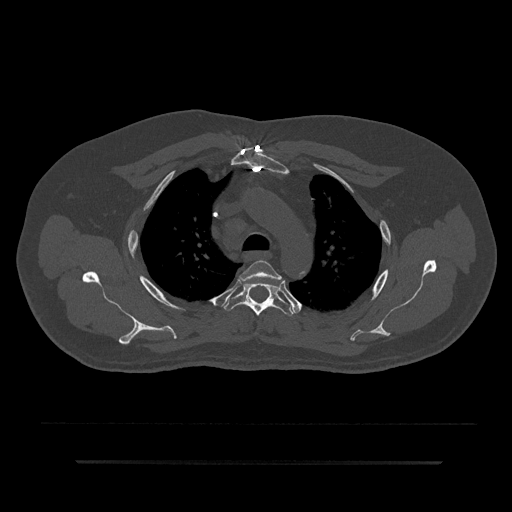
CT including the spine, one axial slice. Position 630 of 797 along the scan axis. Reconstruction kernel Br40s/3. 120 kVp. Bone window (W 1800 / L 400 HU). 512 × 512 image matrix, field of view 464 × 464 mm. Patient: male, 59 years. From the clinical record (not read from this slice): primary cancer: bile ducts.
Annotated regions visible in this slice (semi-automatically segmented with operator editing):
- T3 vertebra: bounding box [x1, y1, x2, y2] px = [240, 260, 283, 283]
- T4 vertebra: [222, 282, 294, 316]